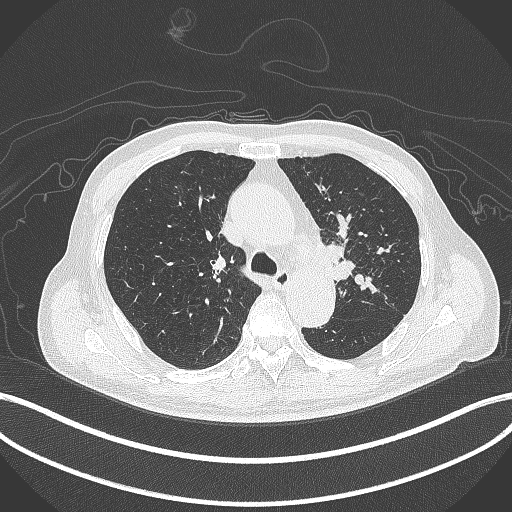
Chest CT, one axial slice. Slice 302 of 417 in the series (ordered by position). 120 kVp. Lung window (W 1500 / L -600 HU). 1 mm slice thickness. 512 × 512 image matrix, field of view 400 × 400 mm. Patient: male, 77 years. From the clinical record (not read from this slice): clinical TNM (as recorded): T3 N1 M0.
Annotated regions visible in this slice (bounding box drawn by a radiologist):
- lung tumour (recorded histology: adenocarcinoma): bounding box [x1, y1, x2, y2] px = [325, 237, 354, 286]